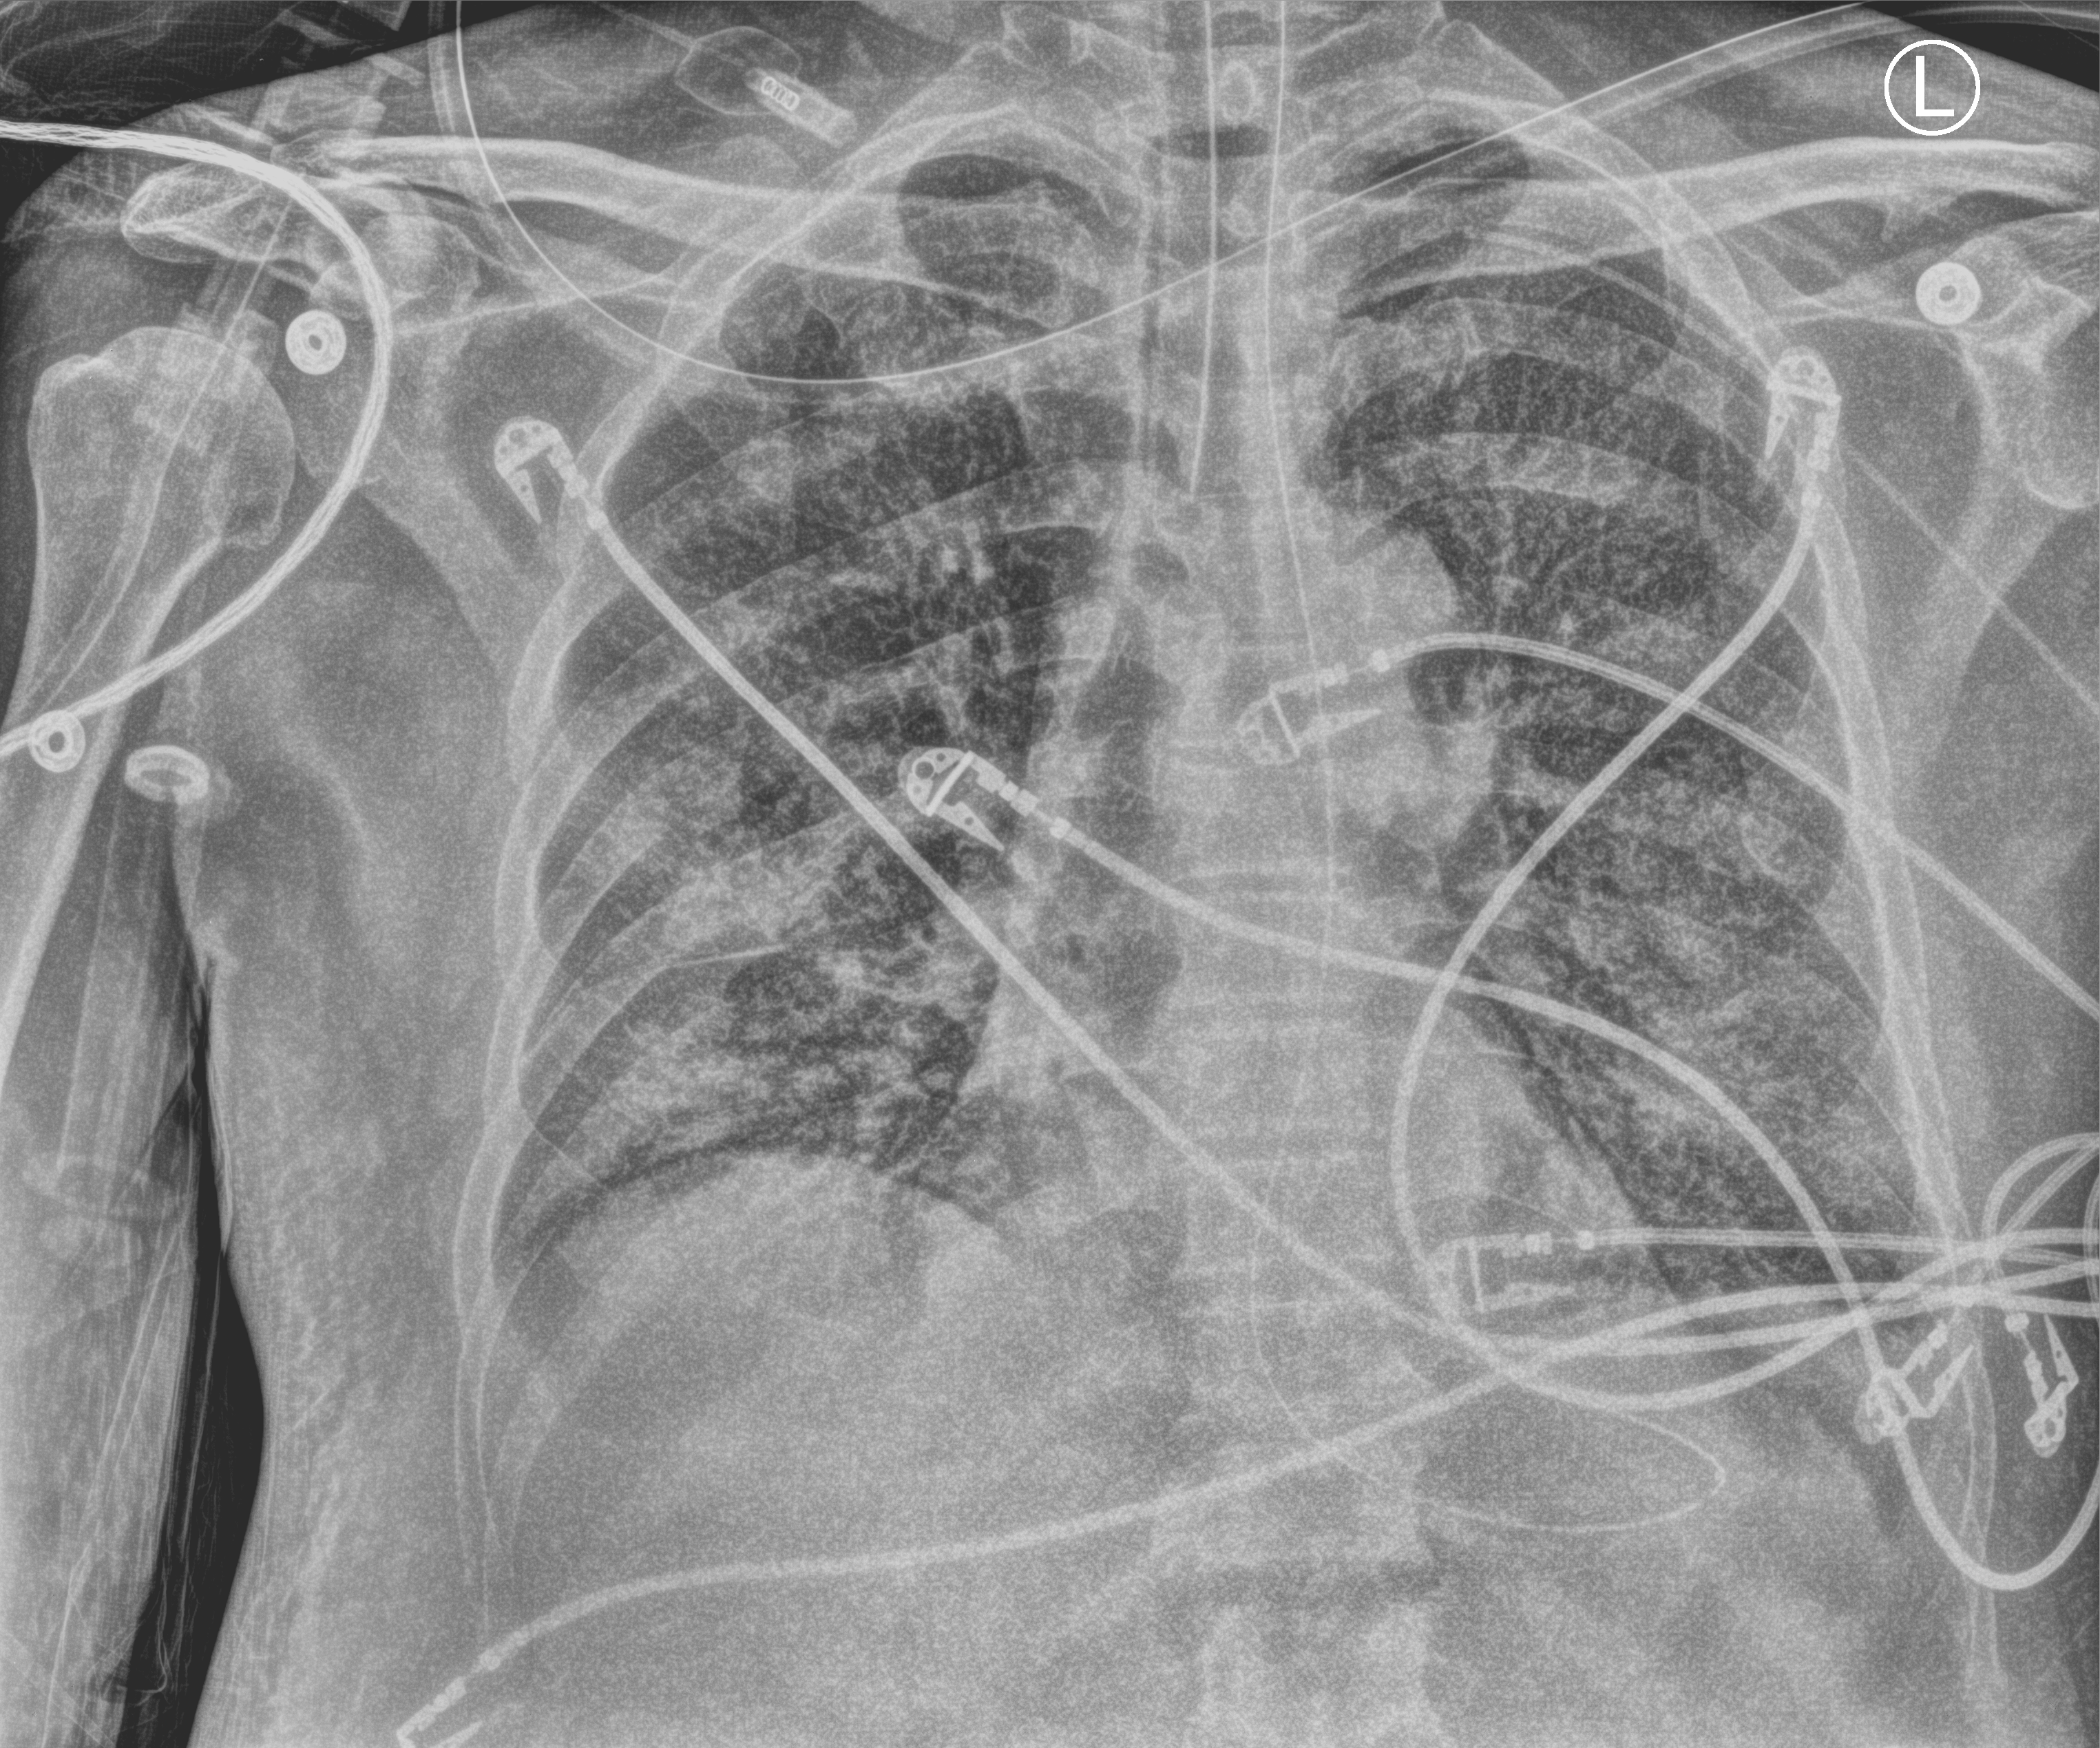
Bedside chest radiograph (computed radiography), anteroposterior (AP) projection. Male patient hospitalised with COVID-19, age 60–74 years.
Hospital-stay facts (about this admission, not read from this image; timing relative to this image not recorded): length of hospital stay: 14 days; hypertension (admission record): yes.